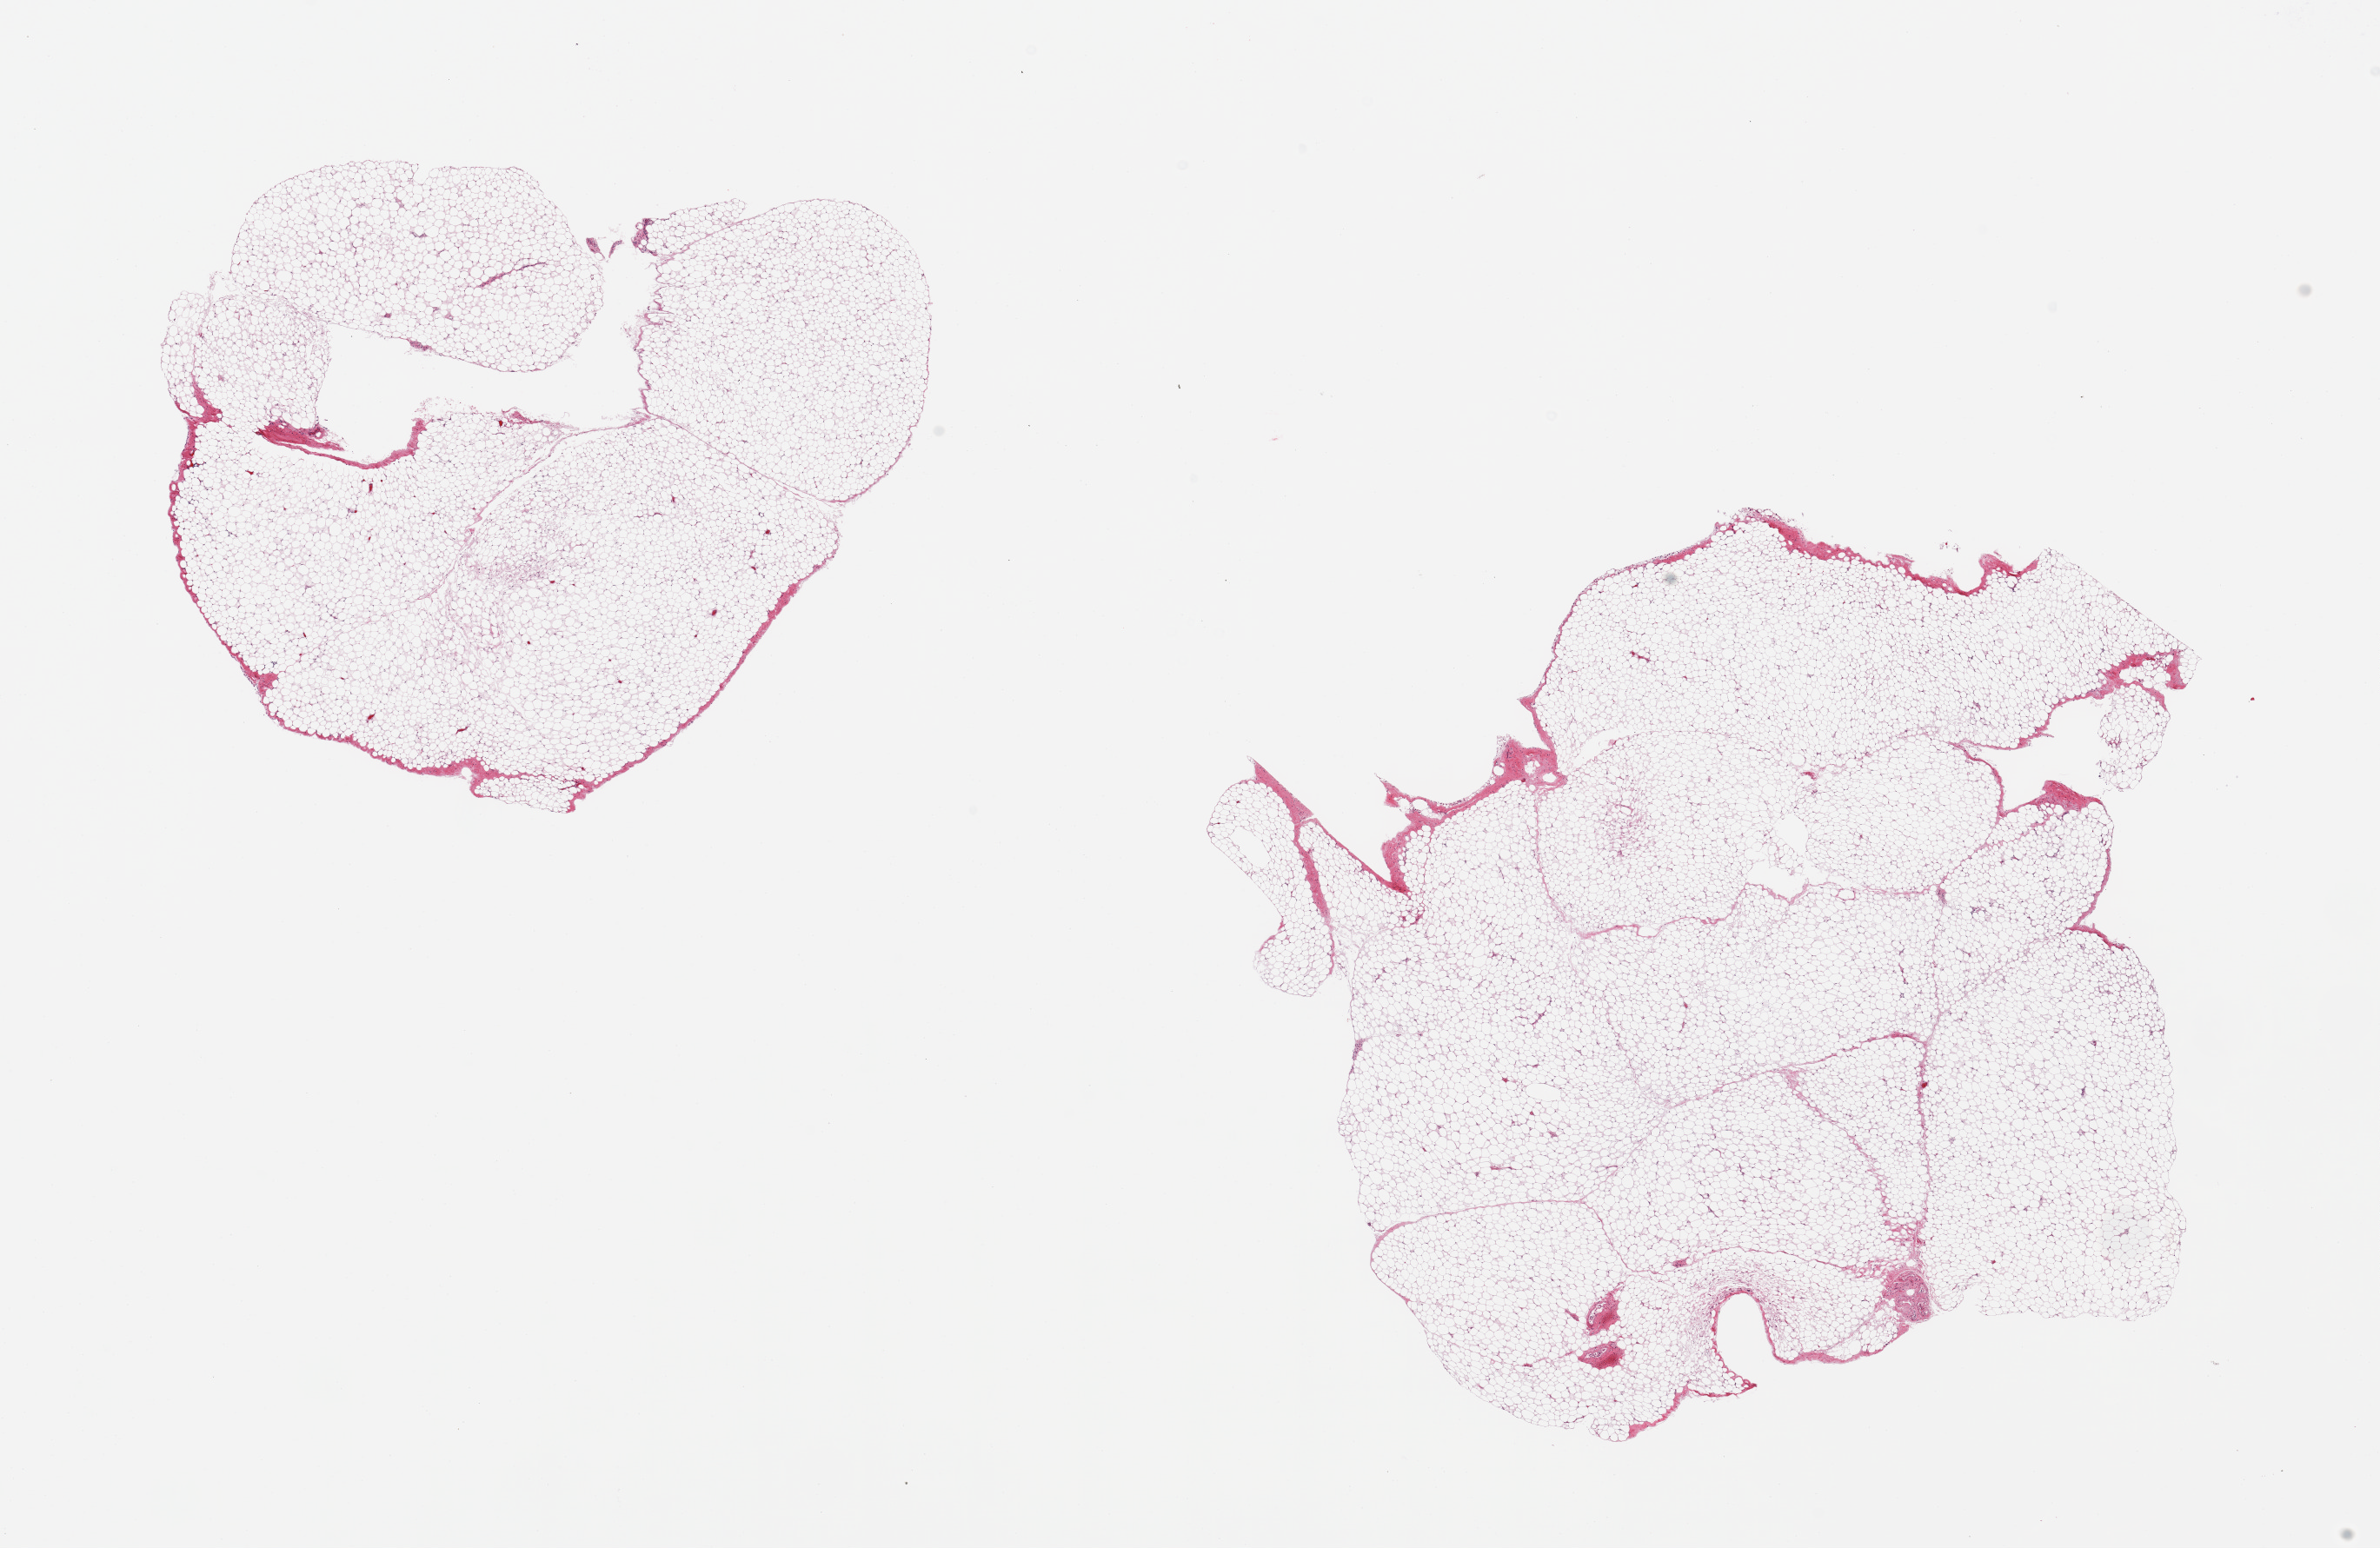
Whole-slide image, haematoxylin and eosin stain, a low-resolution overview of the entire scanned area, about 21.7 x 14.1 mm; PAXgene-fixed, paraffin-embedded tissue; section of omentum (target tissue); donor tissue sample. Female donor.
Reviewer comment on this tissue sample: 2 pieces, minimal fascia.